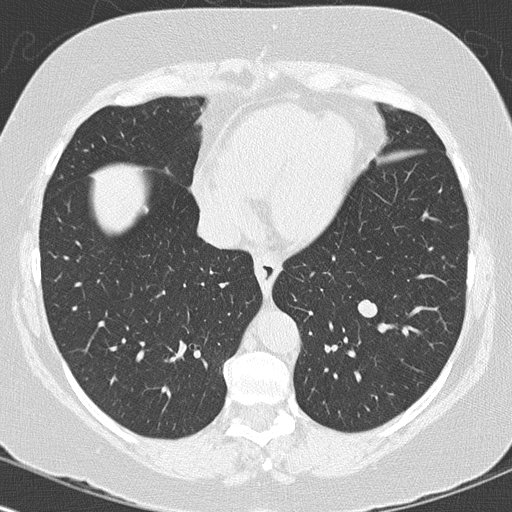
Chest CT (low-dose screening protocol), one axial image; baseline annual screen; lung window (W 1500 / L -600 HU); 2 mm slice thickness; lung (sharp) reconstruction kernel (B50f); 120 kVp; 512 × 512 image matrix. Female participant, aged 60 years at enrolment. Former smoker at enrolment.
Lesion marked by an expert reader, bounding box [x1, y1, x2, y2] px = [348, 291, 389, 329]. Reader record for this screening exam (exam-level; its link to the box is not recorded): non-calcified nodule or mass ≥4 mm, left lower lobe, 12 × 10 mm, smooth margins, soft tissue attenuation. Official screen result: positive, change unspecified: nodule(s) >= 4 mm or enlarging nodule(s), mass(es), or other non-specific abnormalities suspicious for lung cancer. Lung cancer was diagnosed 109 days after this screen: carcinoid tumor, NOS, left lower lobe, carcinoid, stage not assessed, 13 mm at pathology.